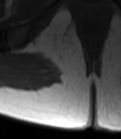
MRI of an extremity soft-tissue mass, one axial slice. Slice 33 of 47 in the series (ordered by position). MR volume resampled by the dataset authors to the PET/CT grid (not the native acquisition matrix). 121 × 139 image matrix, field of view 118 × 136 mm. Female patient. From the clinical record (not read from this slice): histological type: epithelioid sarcoma; grade: intermediate; site of the primary tumour: right buttock.
Outlined on this slice (expert contour drawn on MRI and transferred to this co-registered scan by the dataset authors):
- gross tumour volume including surrounding oedema: bounding box [x1, y1, x2, y2] px = [47, 27, 71, 53]